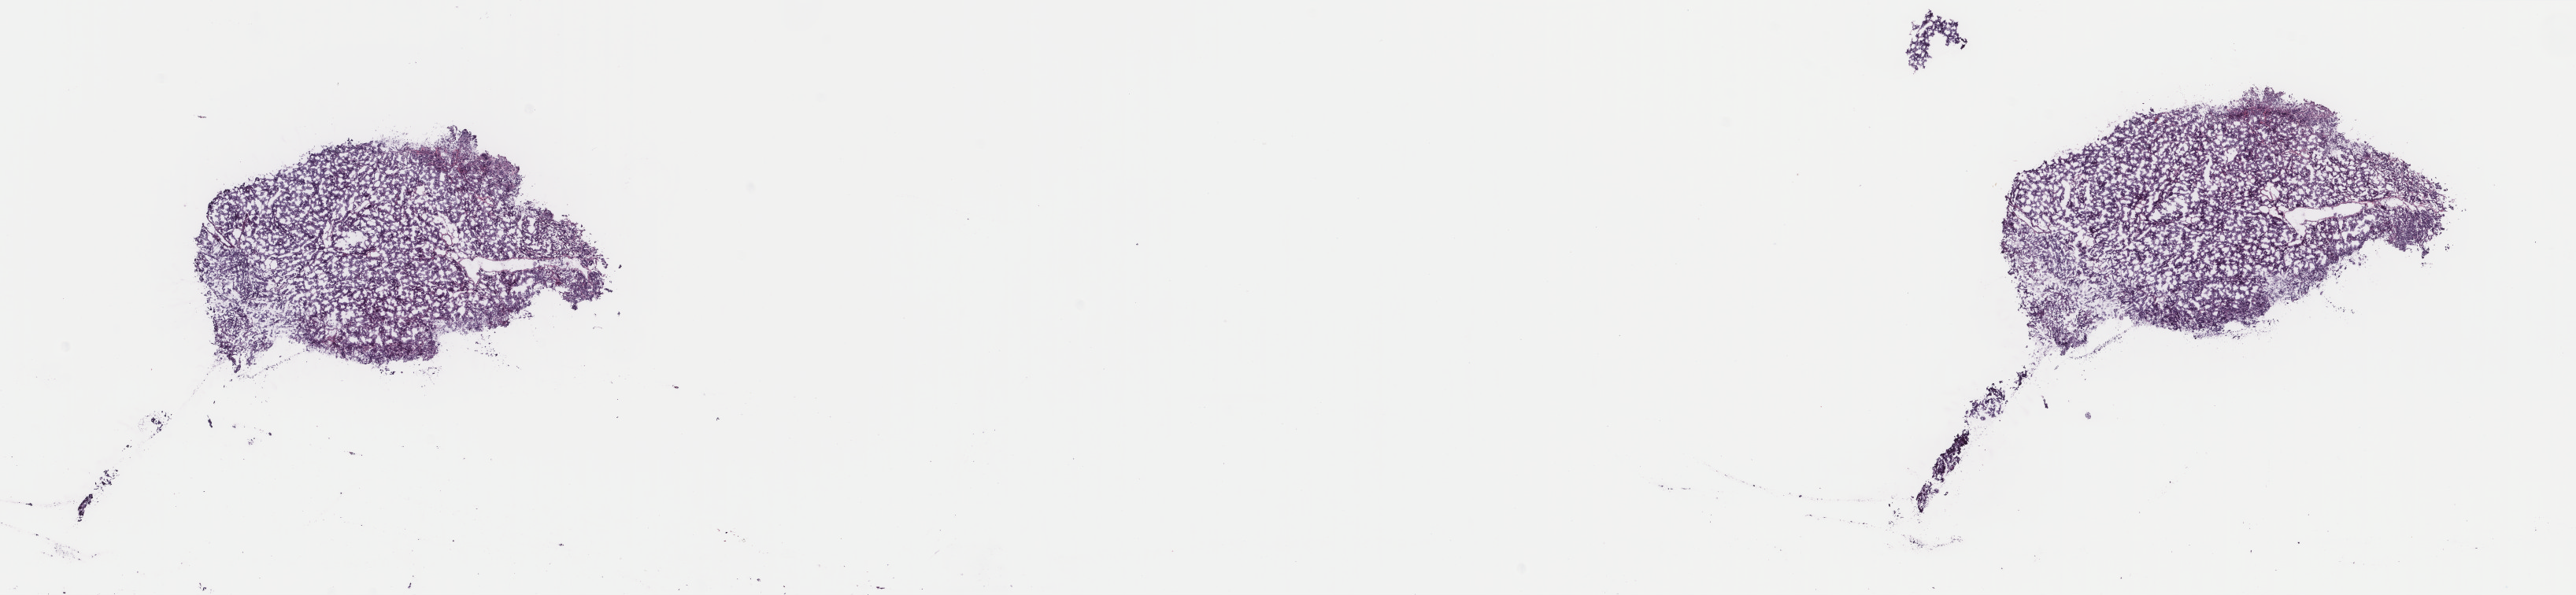
H&E whole-slide image — low-resolution overview of the scanned area, about 26.0 x 6.0 mm (acquisition: 40x scan). Frozen section from the top of the tissue portion. Thyroid, primary tumour sample. Female patient; age at initial diagnosis 37 years. Slide review estimates, as recorded: tumour cells 80%, tumour nuclei 80%.
Pathologic diagnosis: Papillary carcinoma, follicular variant.